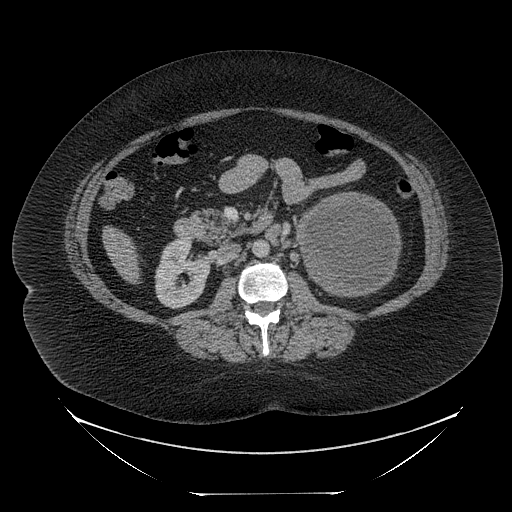
Contrast-enhanced abdominal CT, one axial slice. Position 120 of 205 along the scan axis. Reconstruction kernel STANDARD. 120 kVp. Intravenous contrast given. Soft-tissue window (W 400 / L 40 HU). 512 × 512 image matrix, field of view 500 × 500 mm. Female patient, age 53 years. Case-level facts recorded for this patient, not image findings: diagnosis: adrenocortical carcinoma; tumour side: left adrenal.
Annotated regions visible in this slice (semi-automatically segmented with operator editing):
- mass: bounding box [x1, y1, x2, y2] px = [303, 194, 399, 294]